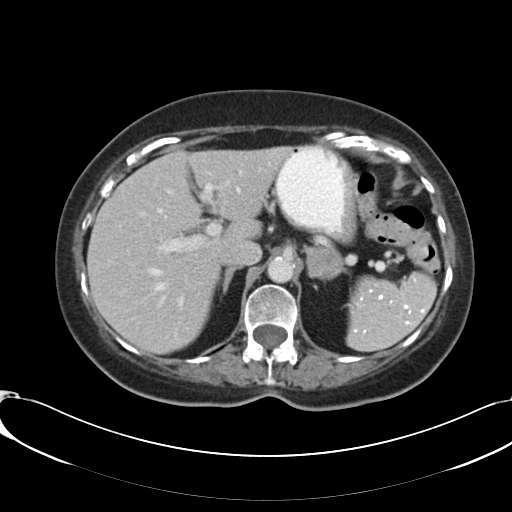
Contrast-enhanced abdominal CT, one axial slice; position 73 of 91 along the scan axis; 120 kVp; intravenous contrast given; soft-tissue window (W 400 / L 40 HU); 5 mm slice thickness; 512 × 512 image matrix, field of view 366 × 366 mm. Female patient, age 73 years. From the clinical record (not read from this slice): diagnosis: adrenocortical carcinoma; tumour side: left adrenal; tumour size at pathology: 4.9 cm; Ki-67 index: 10 %; stage (as recorded): 3.
Annotated regions visible in this slice (semi-automatically segmented with operator editing):
- mass: bounding box <306,248,341,279> (left, top, right, bottom; pixels)